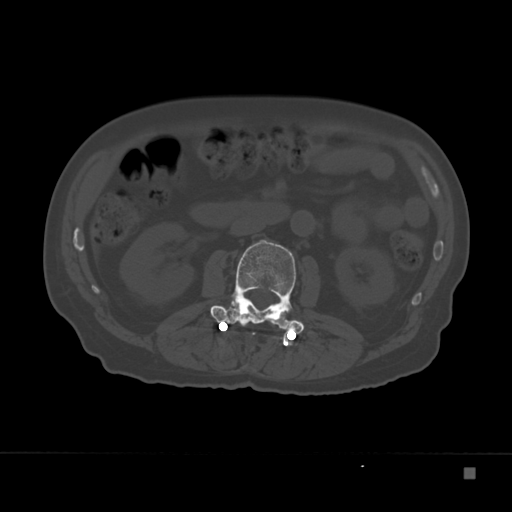
CT including the spine, one axial slice; reconstruction kernel Br40s; 120 kVp; bone window (W 1800 / L 400 HU); 1.5 mm slice thickness; 512 × 512 image matrix, field of view 389 × 389 mm. Patient: male, 72 years. Case-level facts recorded for this patient, not image findings: primary cancer: skeletal.
Annotated regions visible in this slice (semi-automatically segmented with operator editing):
- L2 vertebra: box from (x=211, y=239) to (x=304, y=334) px
- L3 vertebra: (x=225, y=321)–(x=234, y=324)